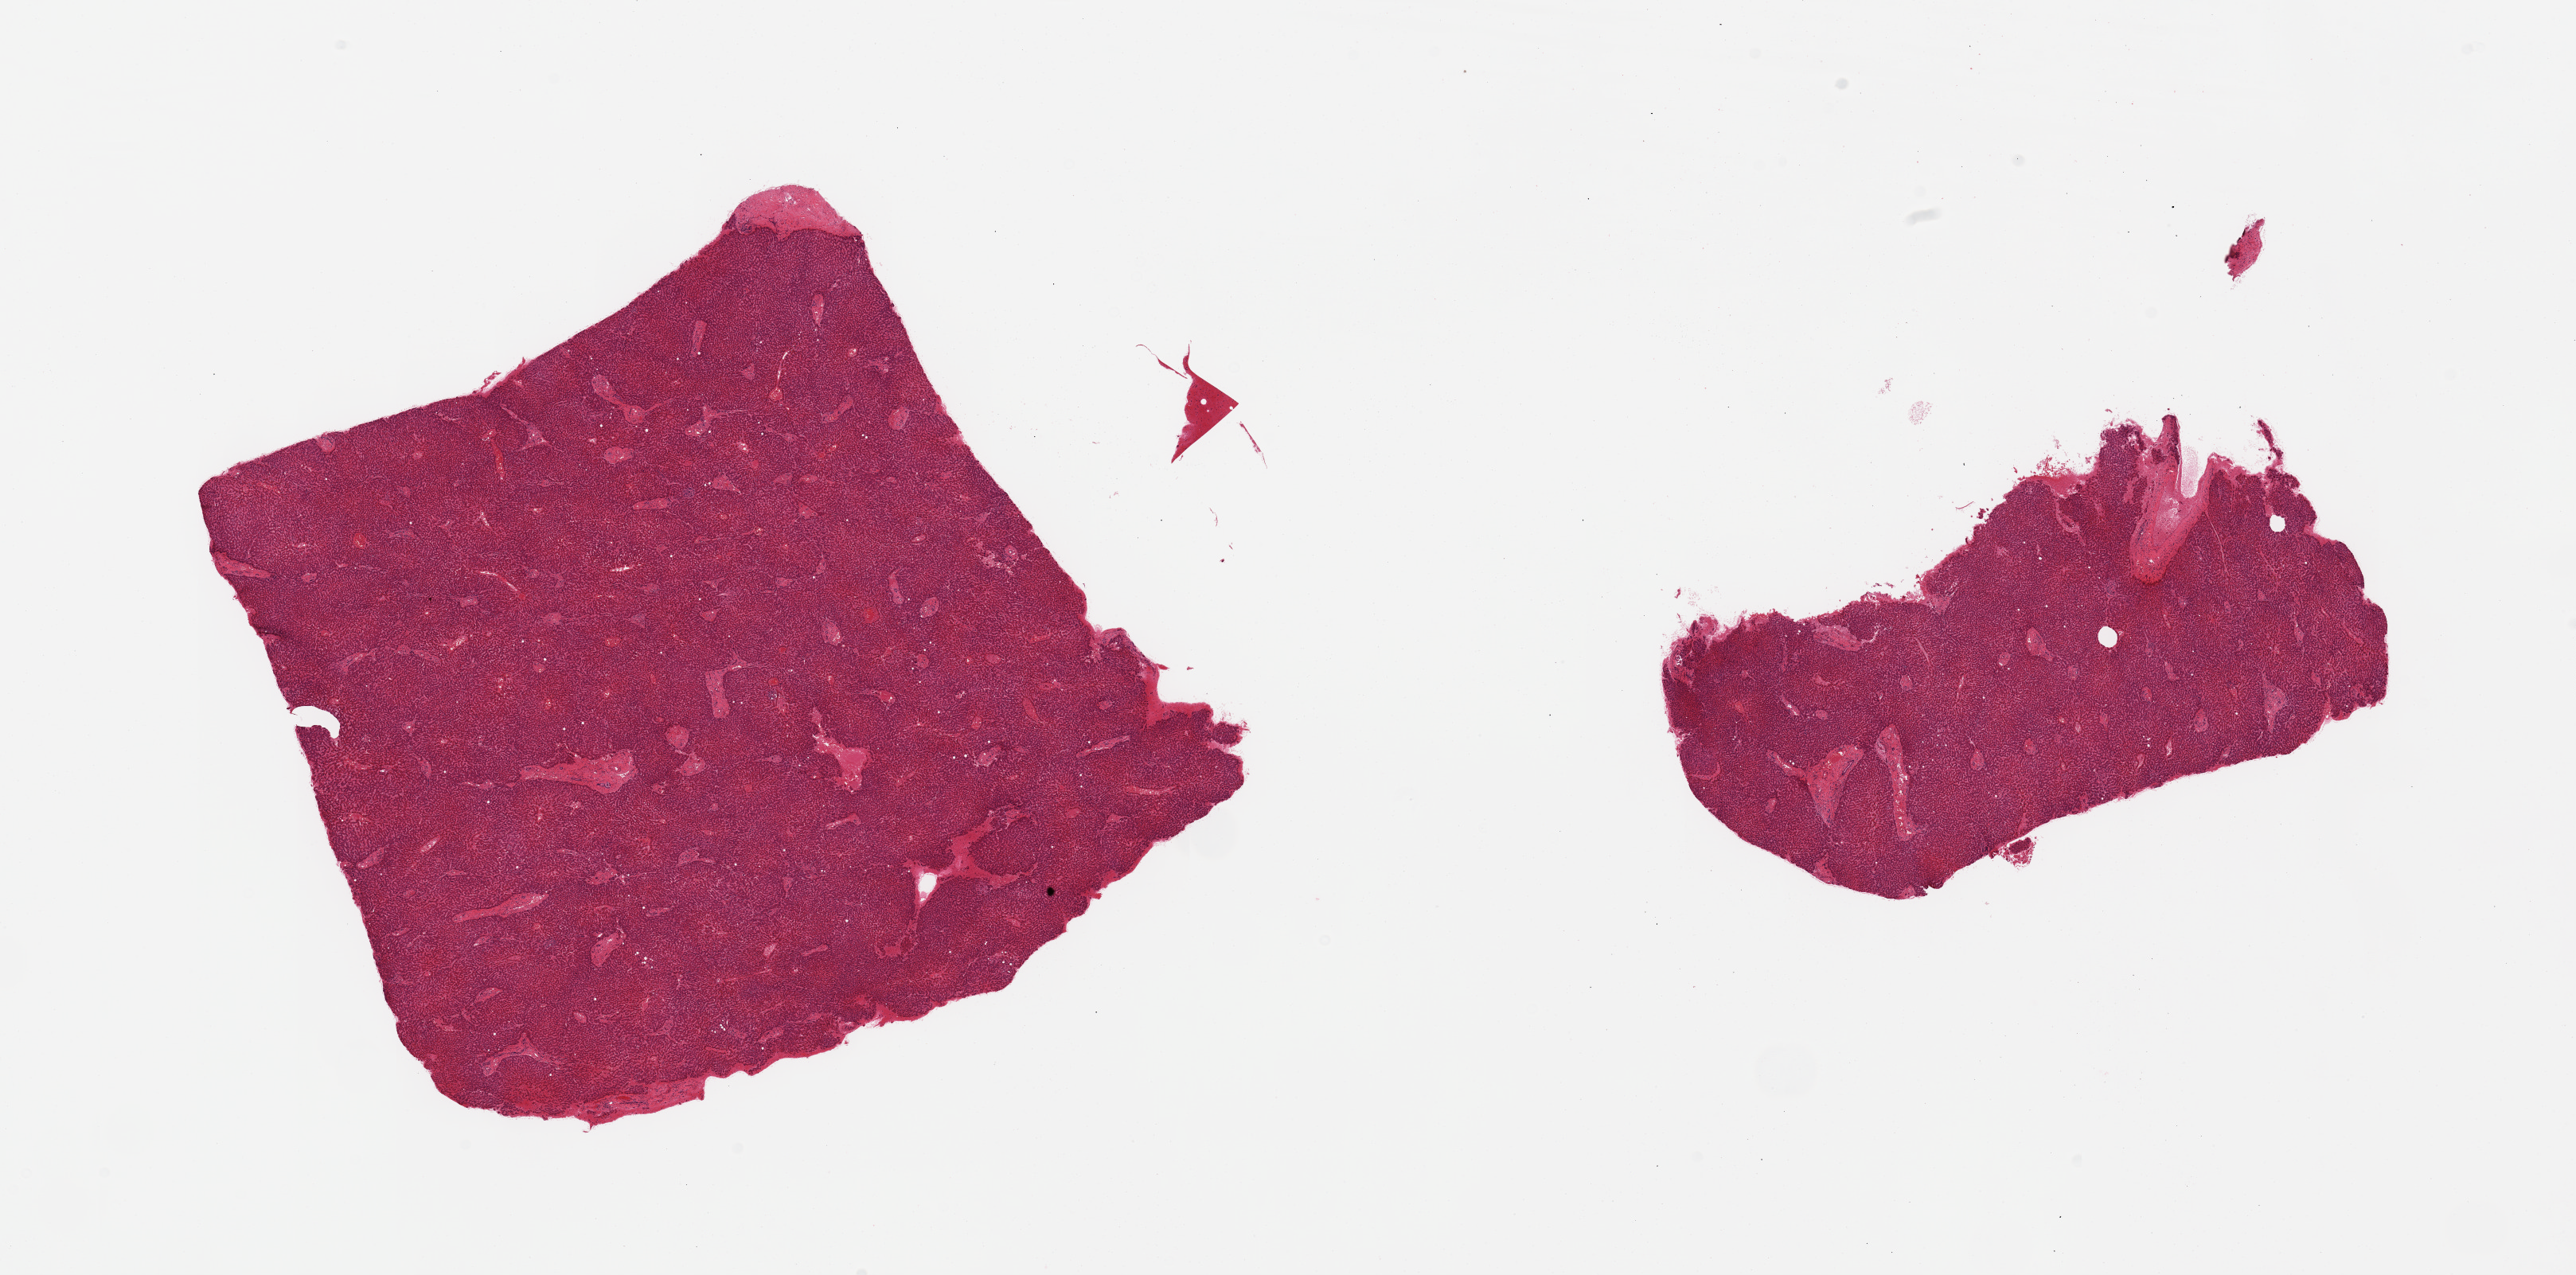
Whole-slide image, hematoxylin and eosin (H&E) stain, brightfield — a low-resolution overview of the entire scanned area, about 25.6 x 12.7 mm, PAXgene-fixed paraffin-embedded (PFPE) section, section of liver (target tissue), tissue donor sample. Donor: male.
* review note (as recorded): 2 pieces, ~5% macrovesicular steatosis